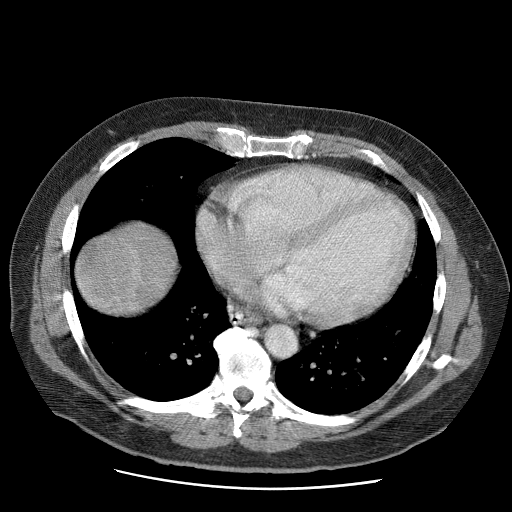
Contrast-enhanced abdominal CT (liver protocol), one axial slice; position 66 of 81 along the scan axis; reconstruction kernel STANDARD; 120 kVp; soft-tissue window (W 400 / L 40 HU); 2.5 mm slice thickness; 512 × 512 image matrix. From the clinical record (not read from this slice): diagnosis: hepatocellular carcinoma (patient treated with transarterial chemoembolisation; whether this scan precedes or follows treatment is not stated here); TNM stage (as recorded): Stage-IIIA; Child-Pugh class: A; tumour differentiation: moderately differentiated; tumour nodularity: multinodular.
Annotated regions visible in this slice (semi-automatically segmented with operator editing):
- liver parenchyma outside the tumour (the mass and vessels are separate outlines, so this box may not span the whole liver): bounding box (x1, y1, x2, y2) in pixels: (76, 222, 176, 314)
- mass: (75, 236, 143, 313)